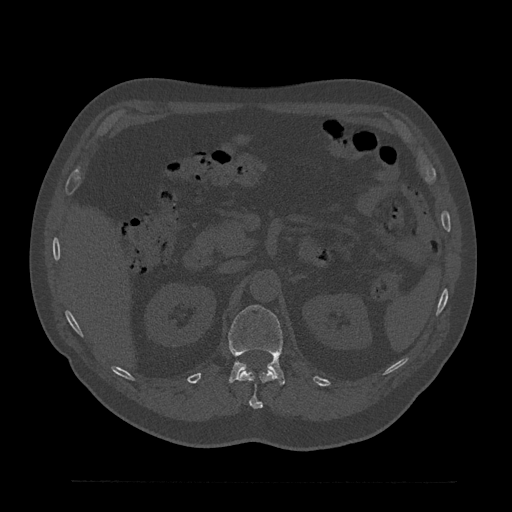
CT including the spine, one axial slice. Position 191 of 797 along the scan axis. Bone window (W 1800 / L 400 HU). 0.5 mm slice thickness. 512 × 512 image matrix. Male patient, age 61 years. From the clinical record (not read from this slice): primary cancer: prostate.
Structures marked on this image (semi-automatically segmented with operator editing):
- L1 vertebra: box from (x=228, y=305) to (x=284, y=385) px
- T12 vertebra: (x=238, y=370)–(x=276, y=409)